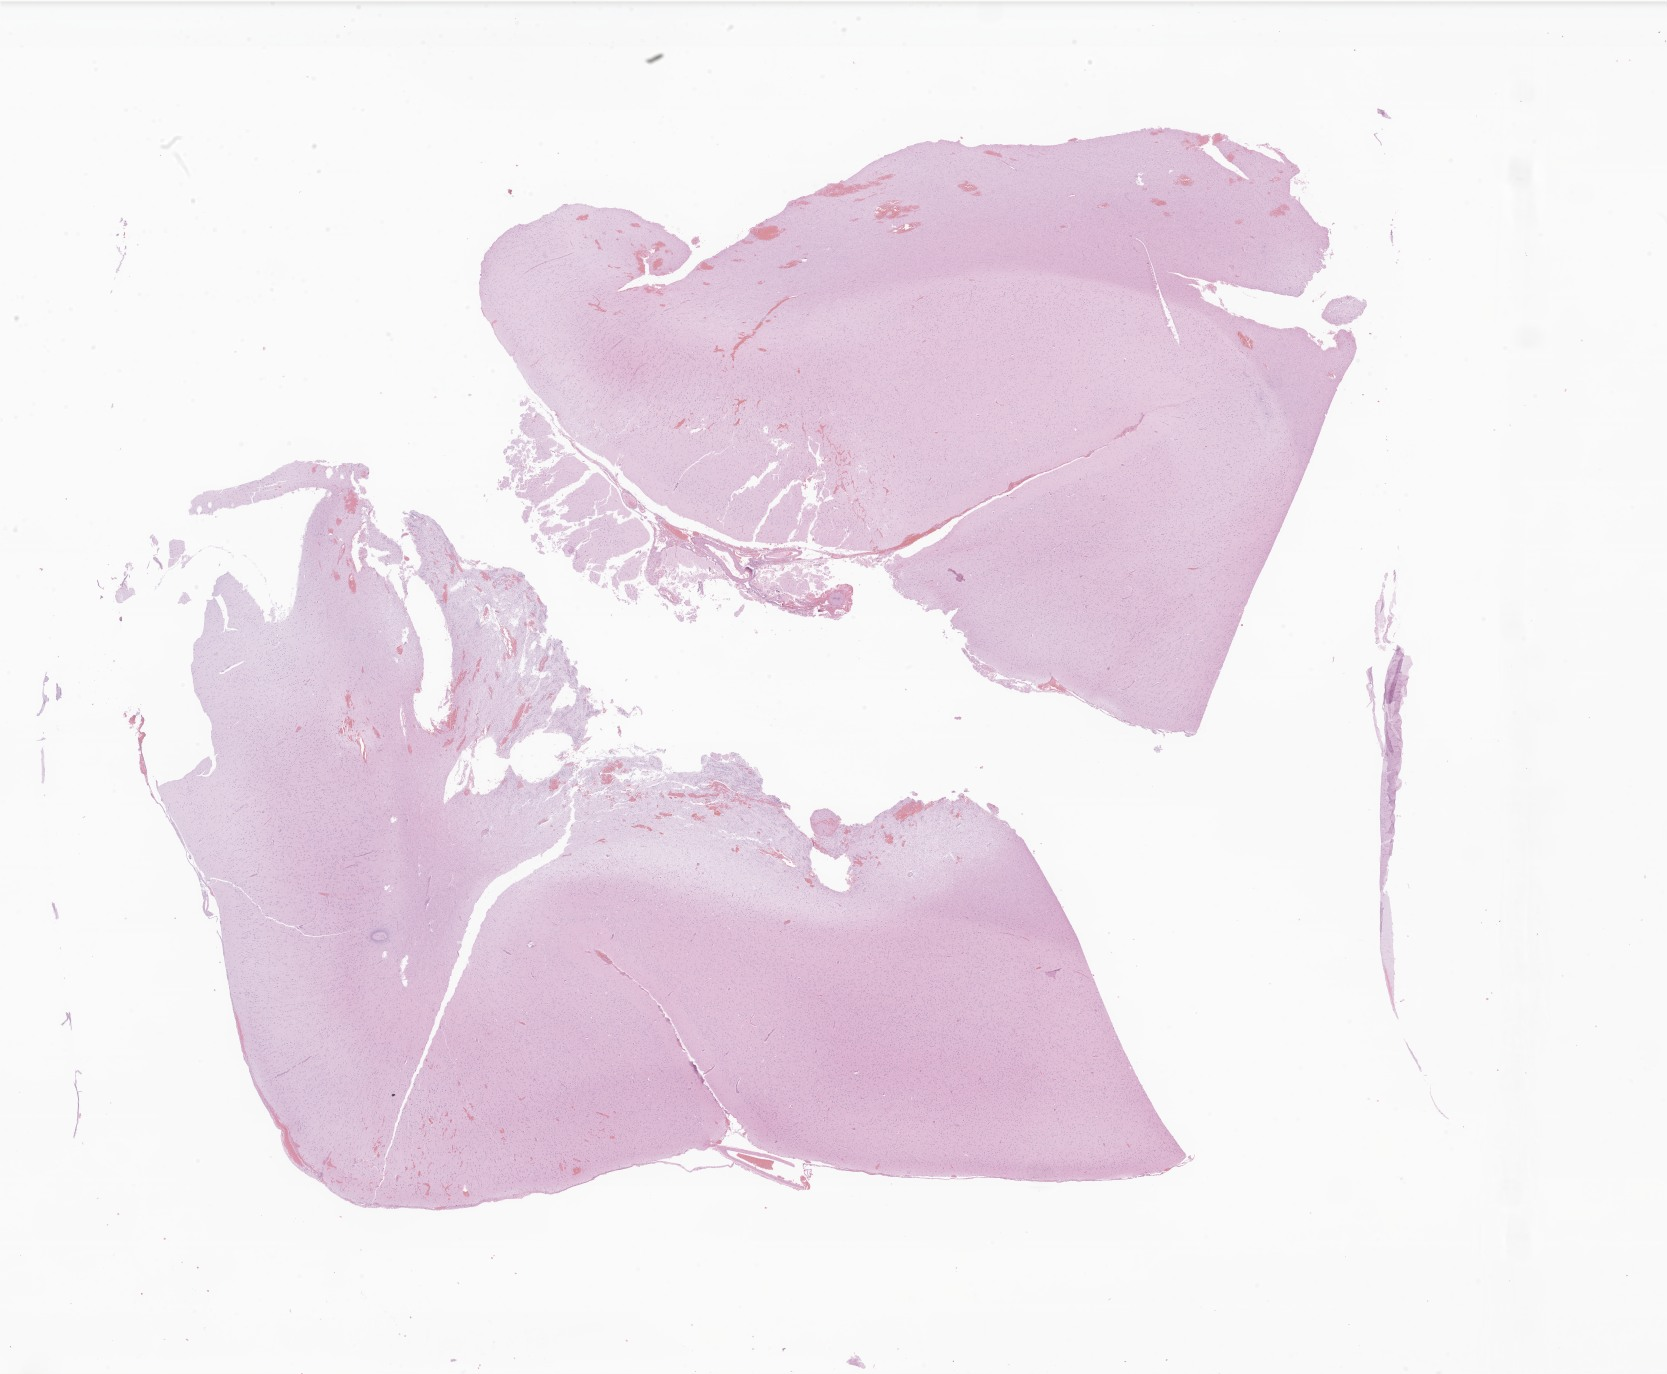
Digitized hematoxylin and eosin (H&E)-stained section of tumor tissue from the brain — shown as a low-resolution overview of the whole scanned area (about 28.1 x 23.2 mm); FFPE section. Patient: male, age 173 months (14 years 5 months).
Diagnosis: Dysembryoplastic neuroepithelial tumor.